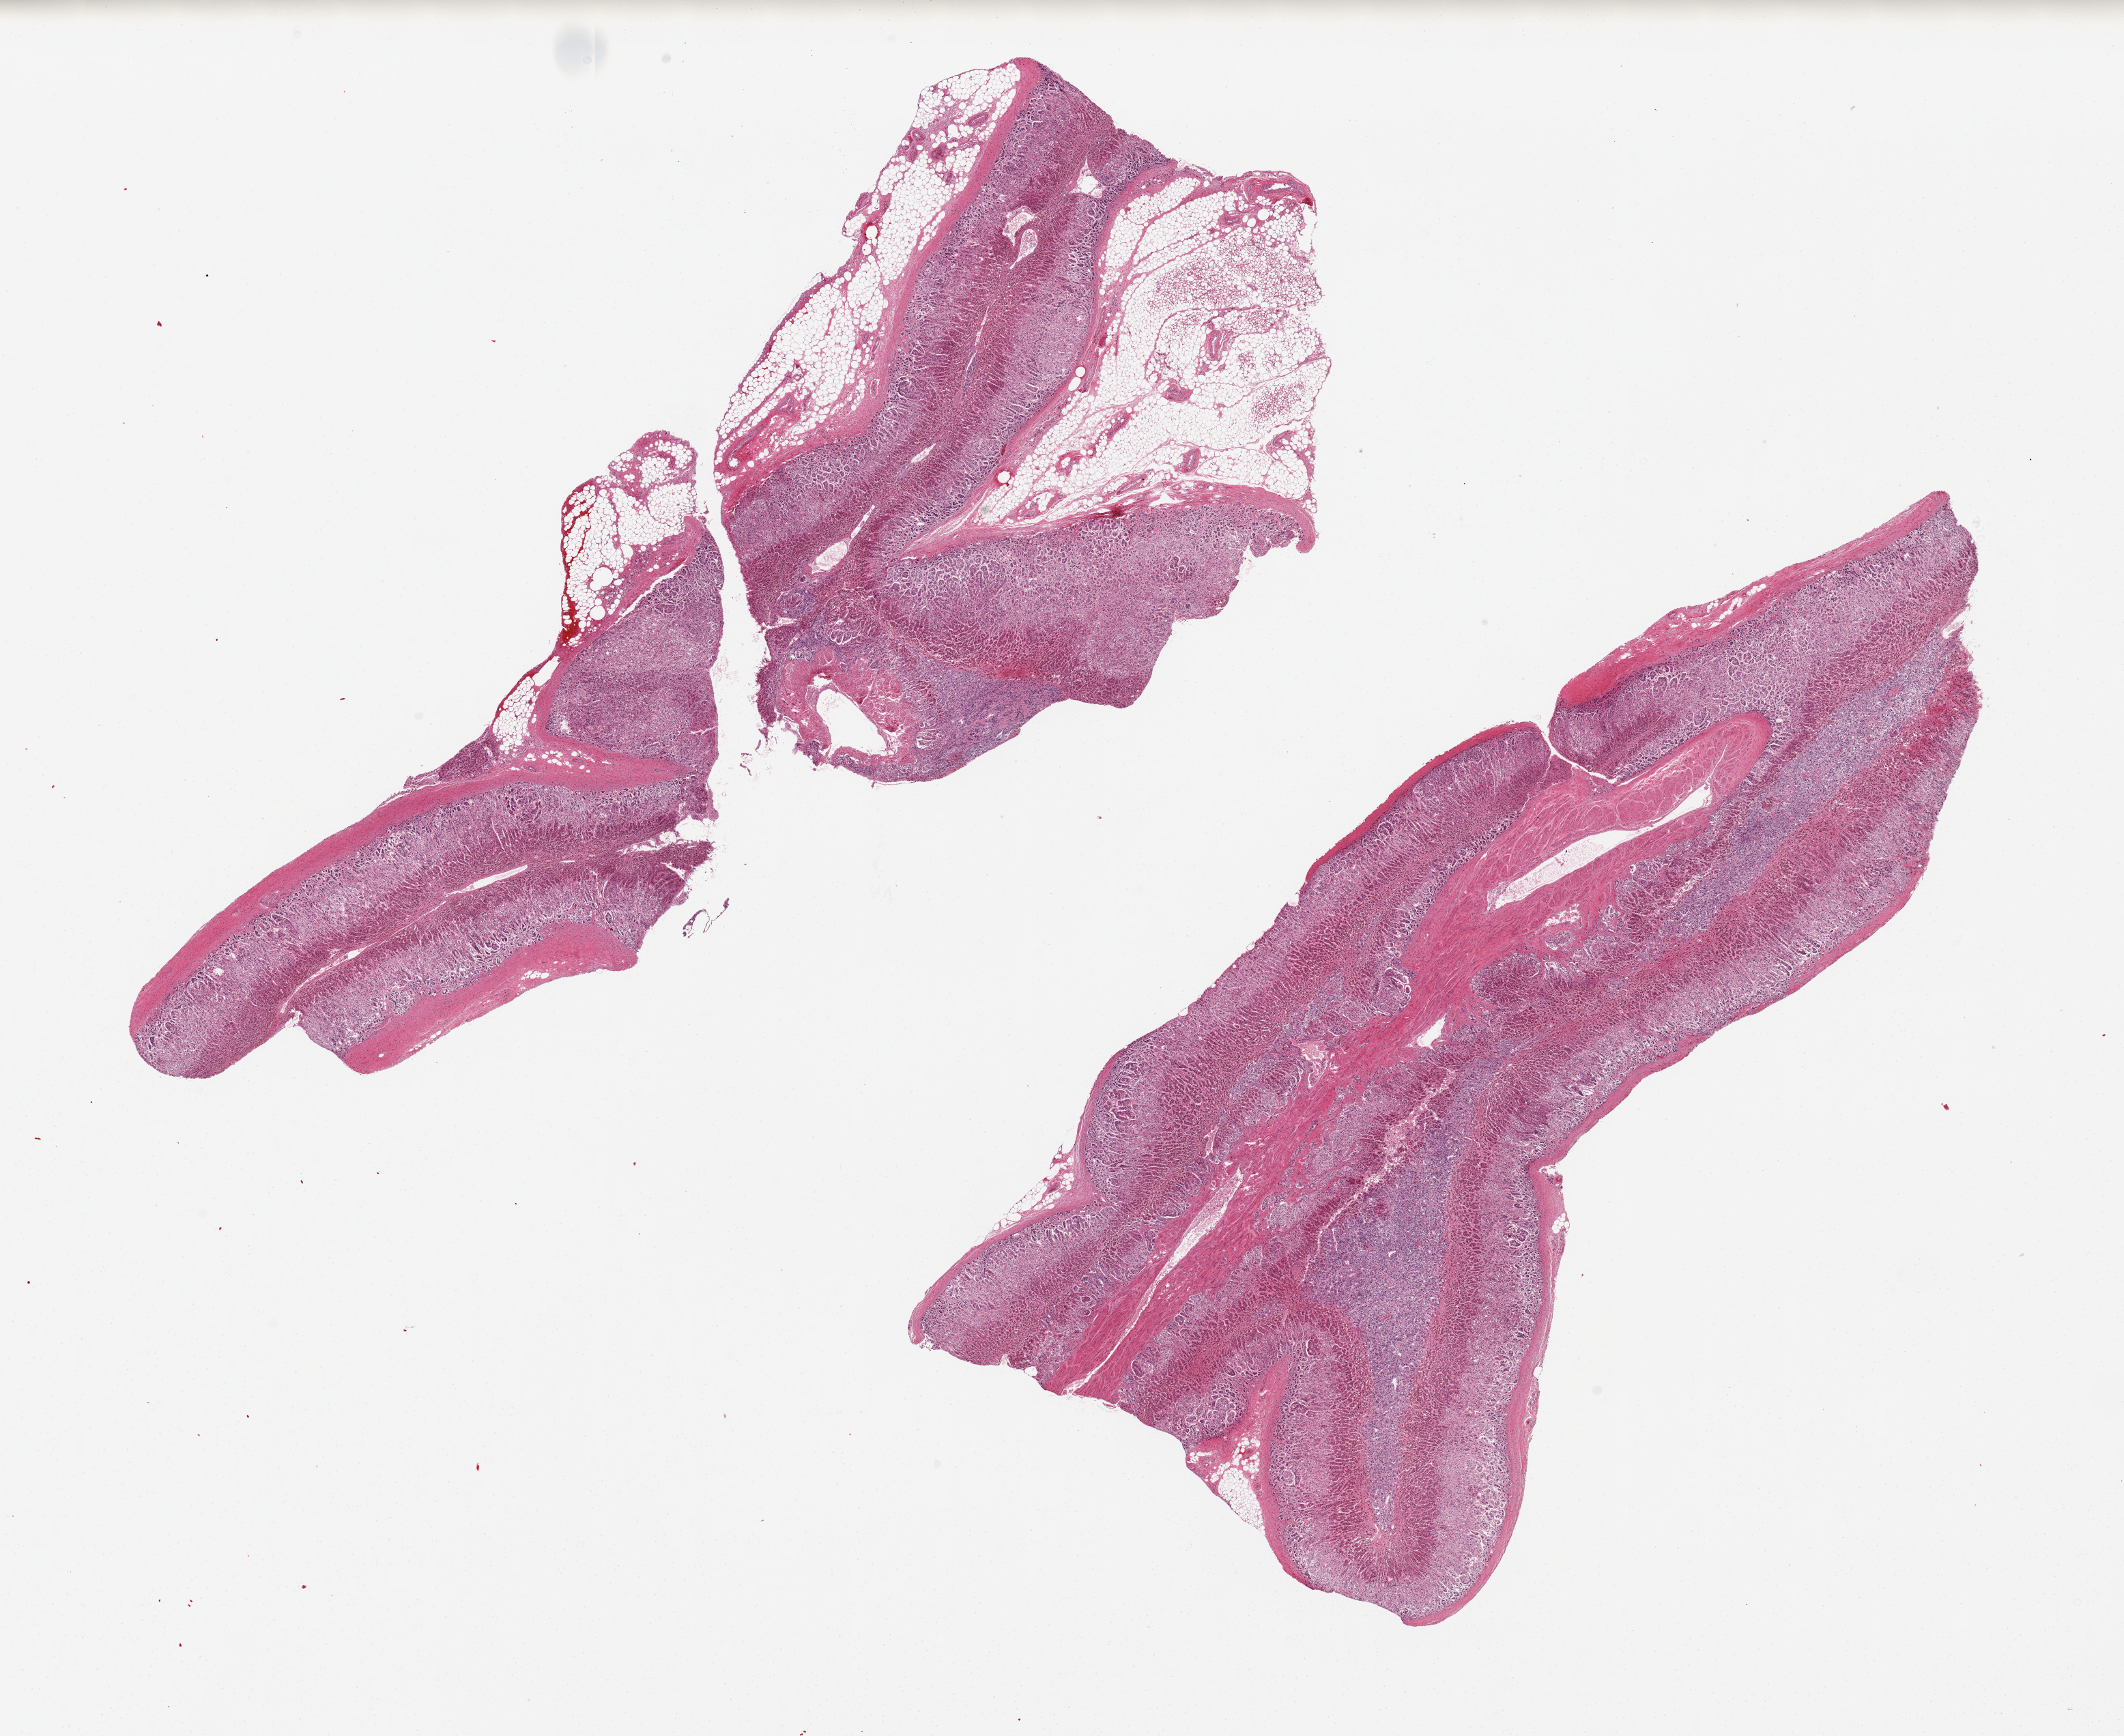
Digitized hematoxylin and eosin (H&E)-stained section, brightfield — shown as a low-resolution overview of the whole scanned area (about 24.6 x 20.1 mm); PAXgene-fixed paraffin-embedded (PFPE) section; section of adrenal gland (target tissue); tissue donor sample.
Pathologist's review note for this sample: 2 pieces, mainly cortex, focal medulla, adherent fat up to ~1-2mm on one aliquot, moderately-severely autolyzed.